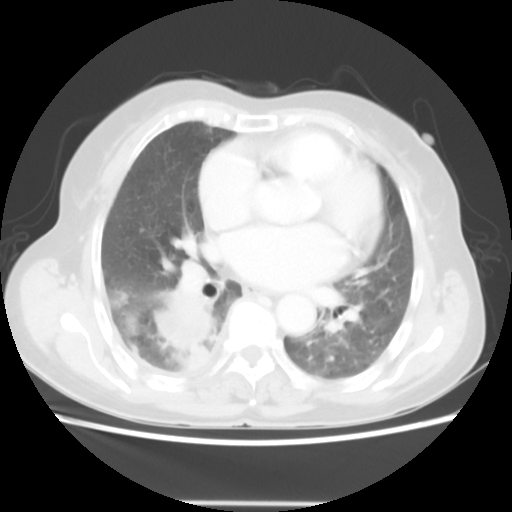
Chest CT, one axial slice. Position 25 of 52 along the scan axis. Reconstruction kernel STANDARD. Lung window (W 1500 / L -600 HU). 5 mm slice thickness. 512 × 512 image matrix. Female patient, age 67 years. Case-level facts recorded for this patient, not image findings: clinical TNM (as recorded): T3 N1 M1.
Annotated regions visible in this slice (bounding box drawn by a radiologist):
- lung tumour (recorded histology: adenocarcinoma): bounding box (x1, y1, x2, y2) in pixels: (154, 288, 219, 375)